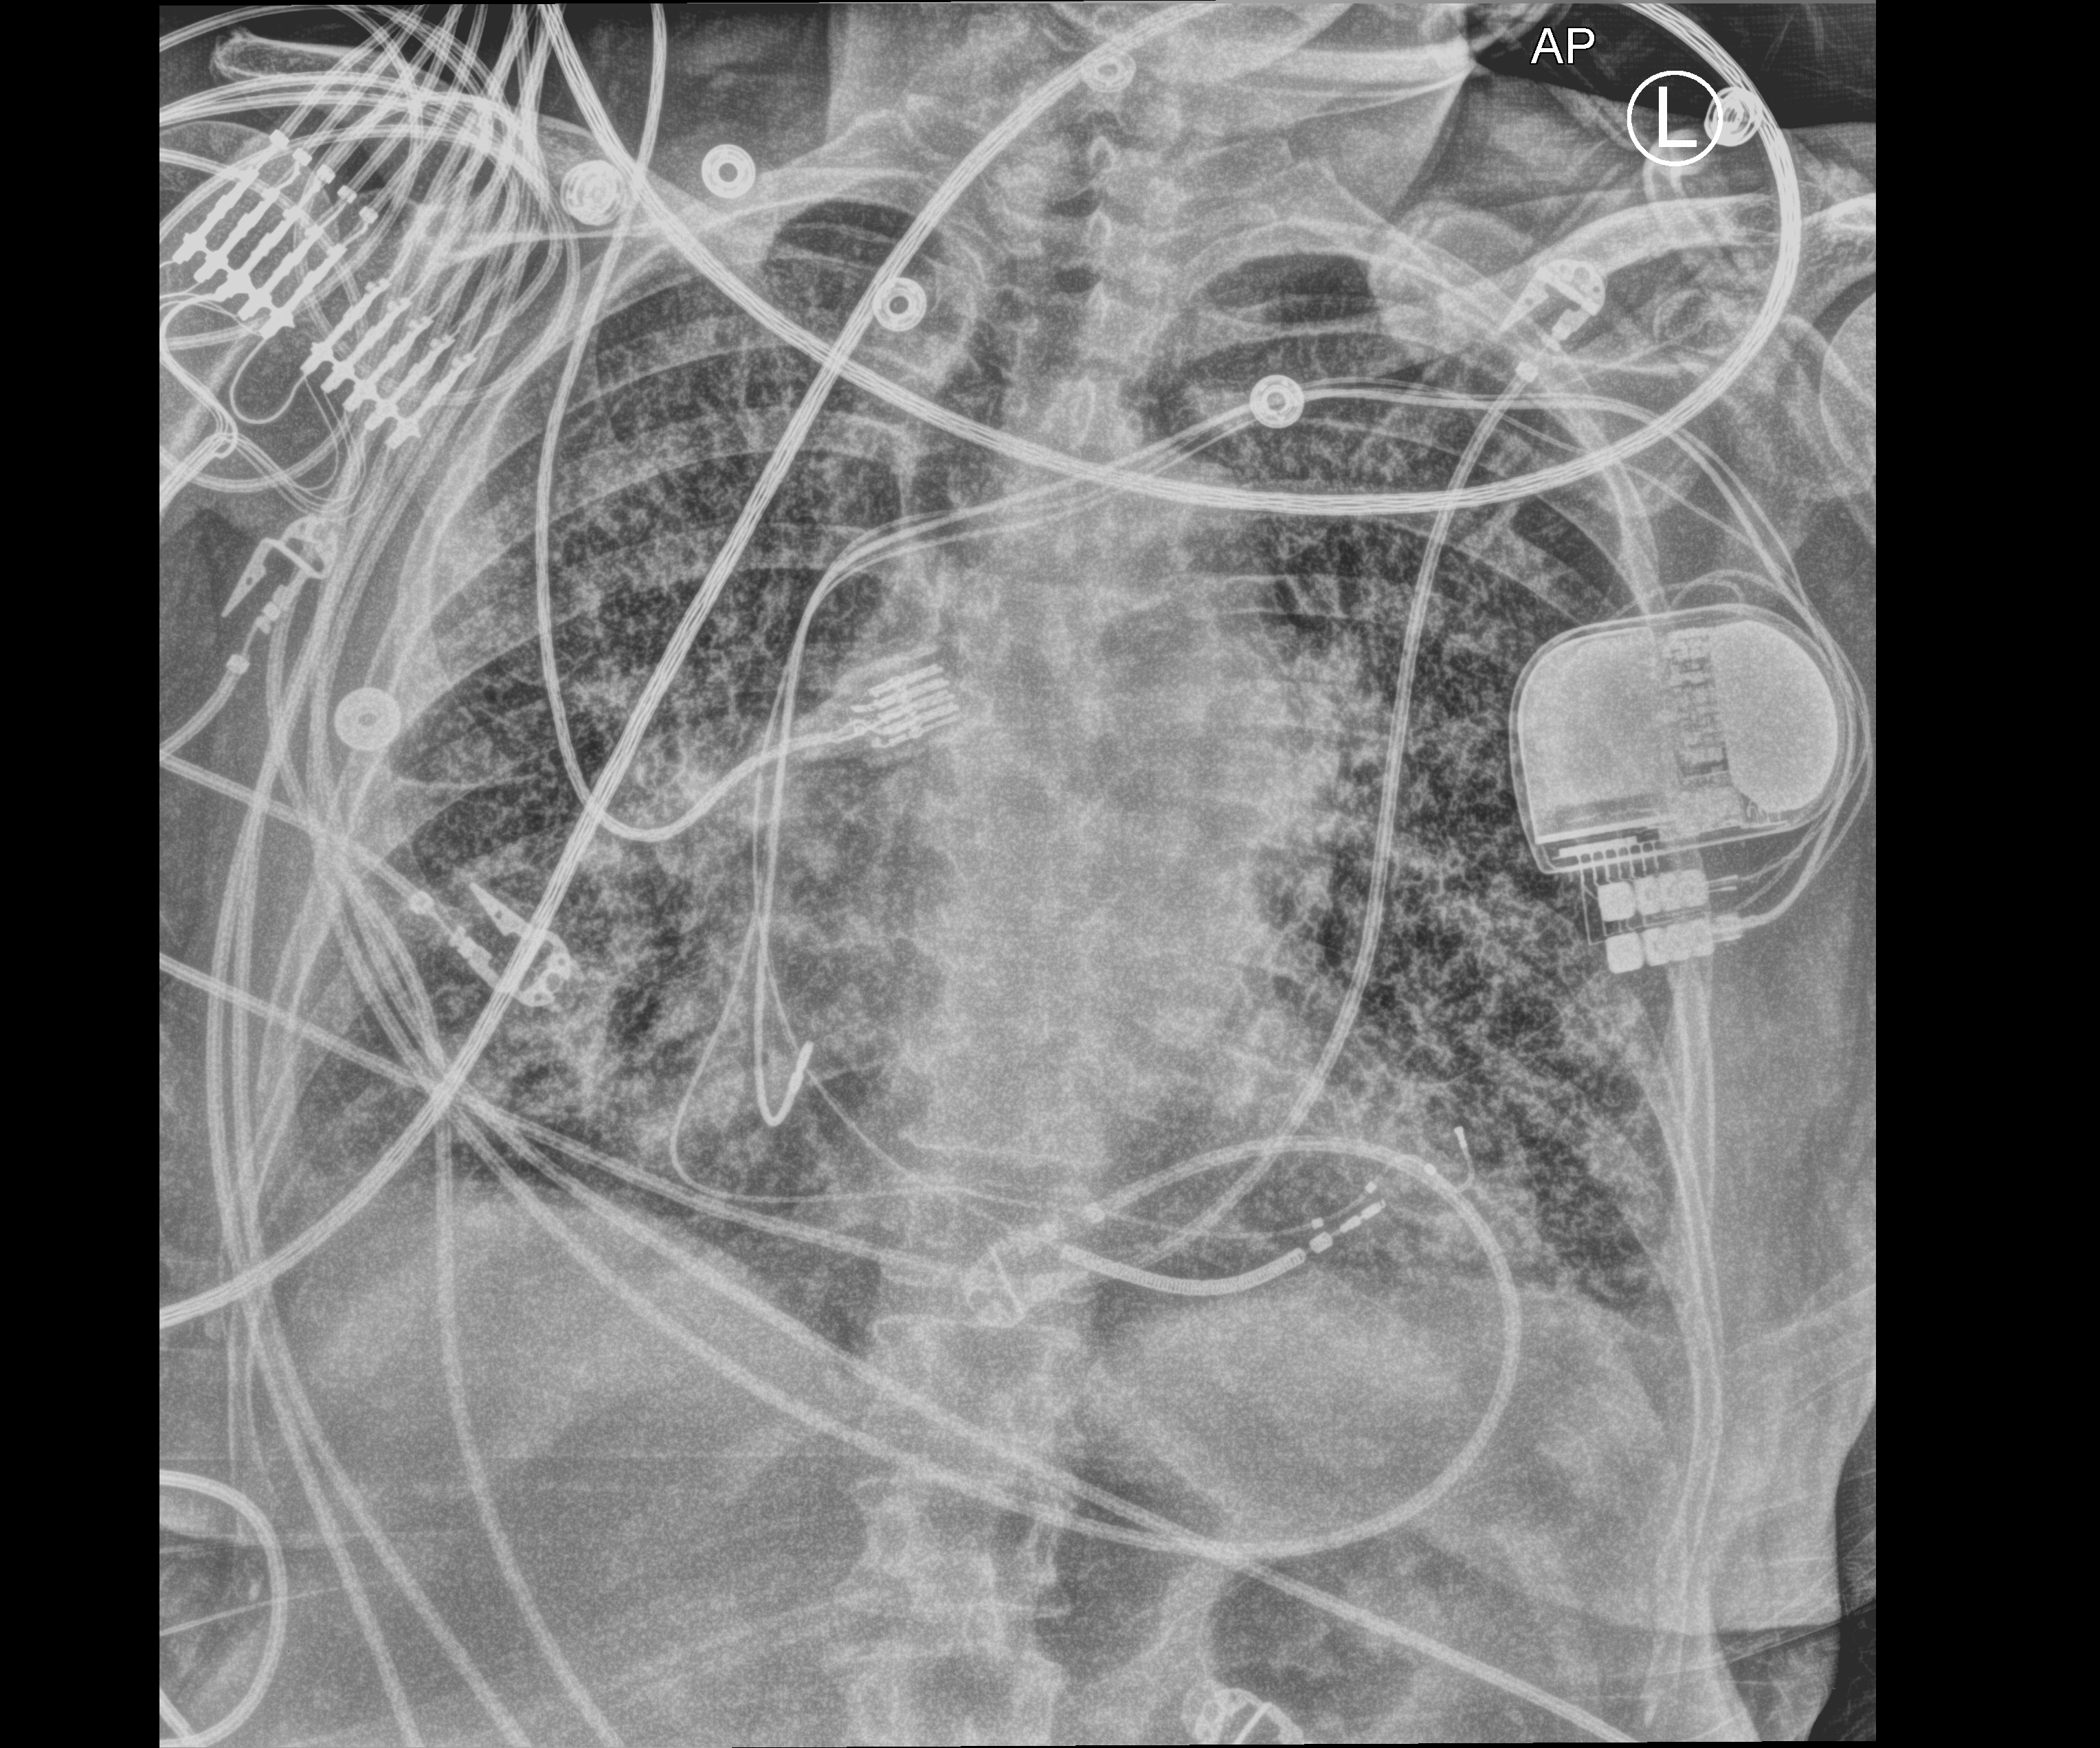
Portable chest radiograph; anteroposterior (AP) projection. Patient hospitalised with COVID-19; female, aged 60–74 years.
Hospital-stay facts (about this admission, not read from this image; timing relative to this image not recorded):
- length of hospital stay: 6 days